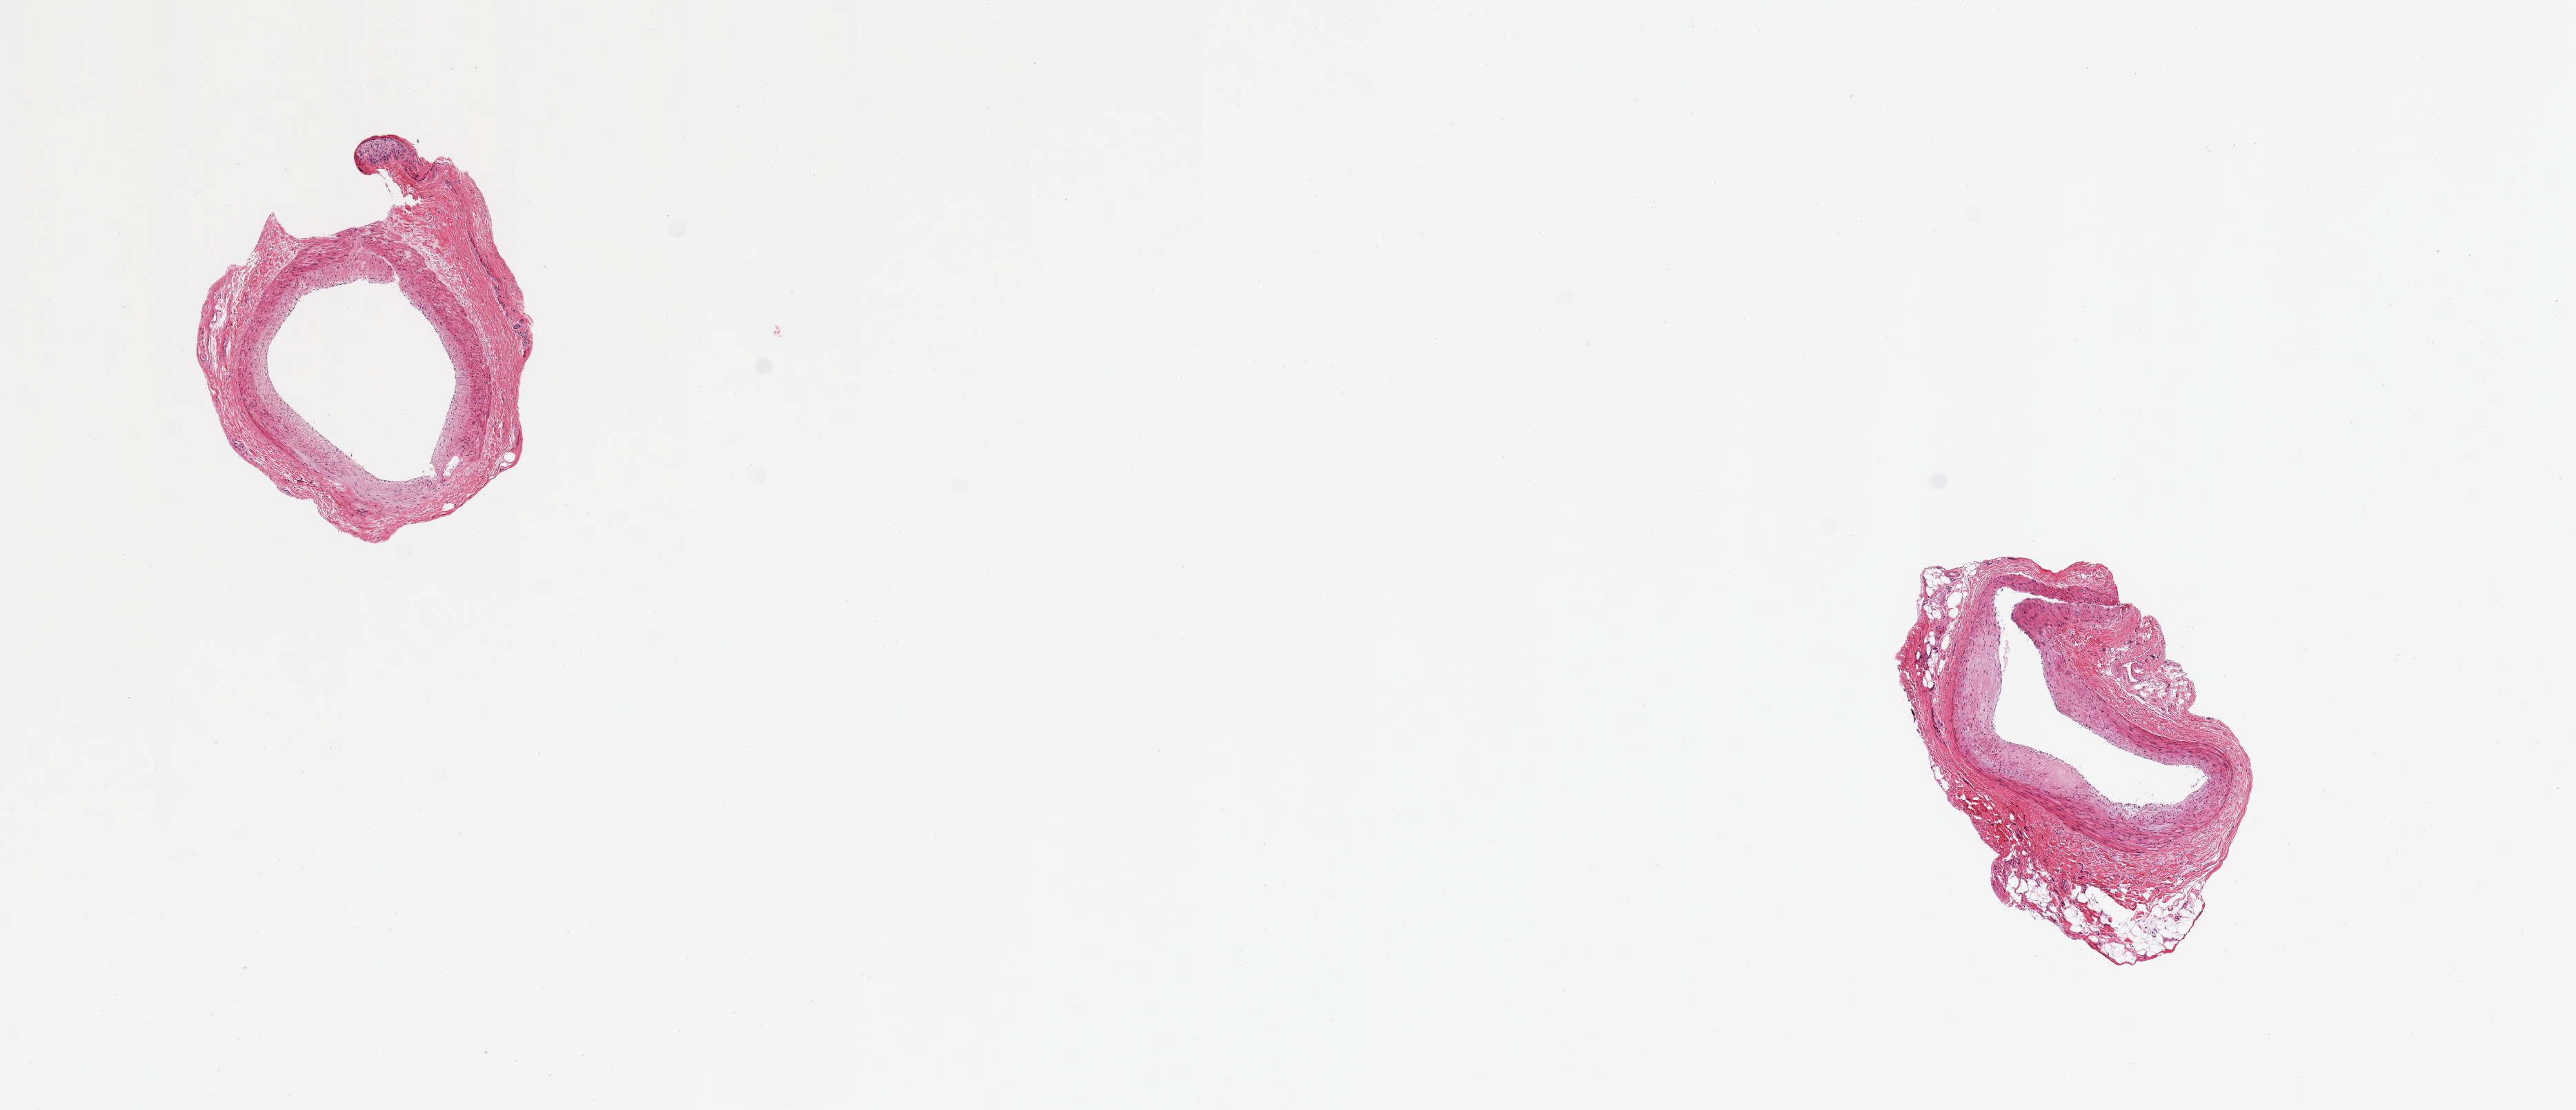
Haematoxylin and eosin whole-slide image — shown as a low-resolution overview of the whole scanned area (about 14.8 x 6.4 mm); PAXgene-fixed, paraffin-embedded tissue; sampled site (target tissue): coronary artery; donor tissue sample.
Review note (as recorded): 2 pieces; mild to moderate plaque formation; well trimmed.